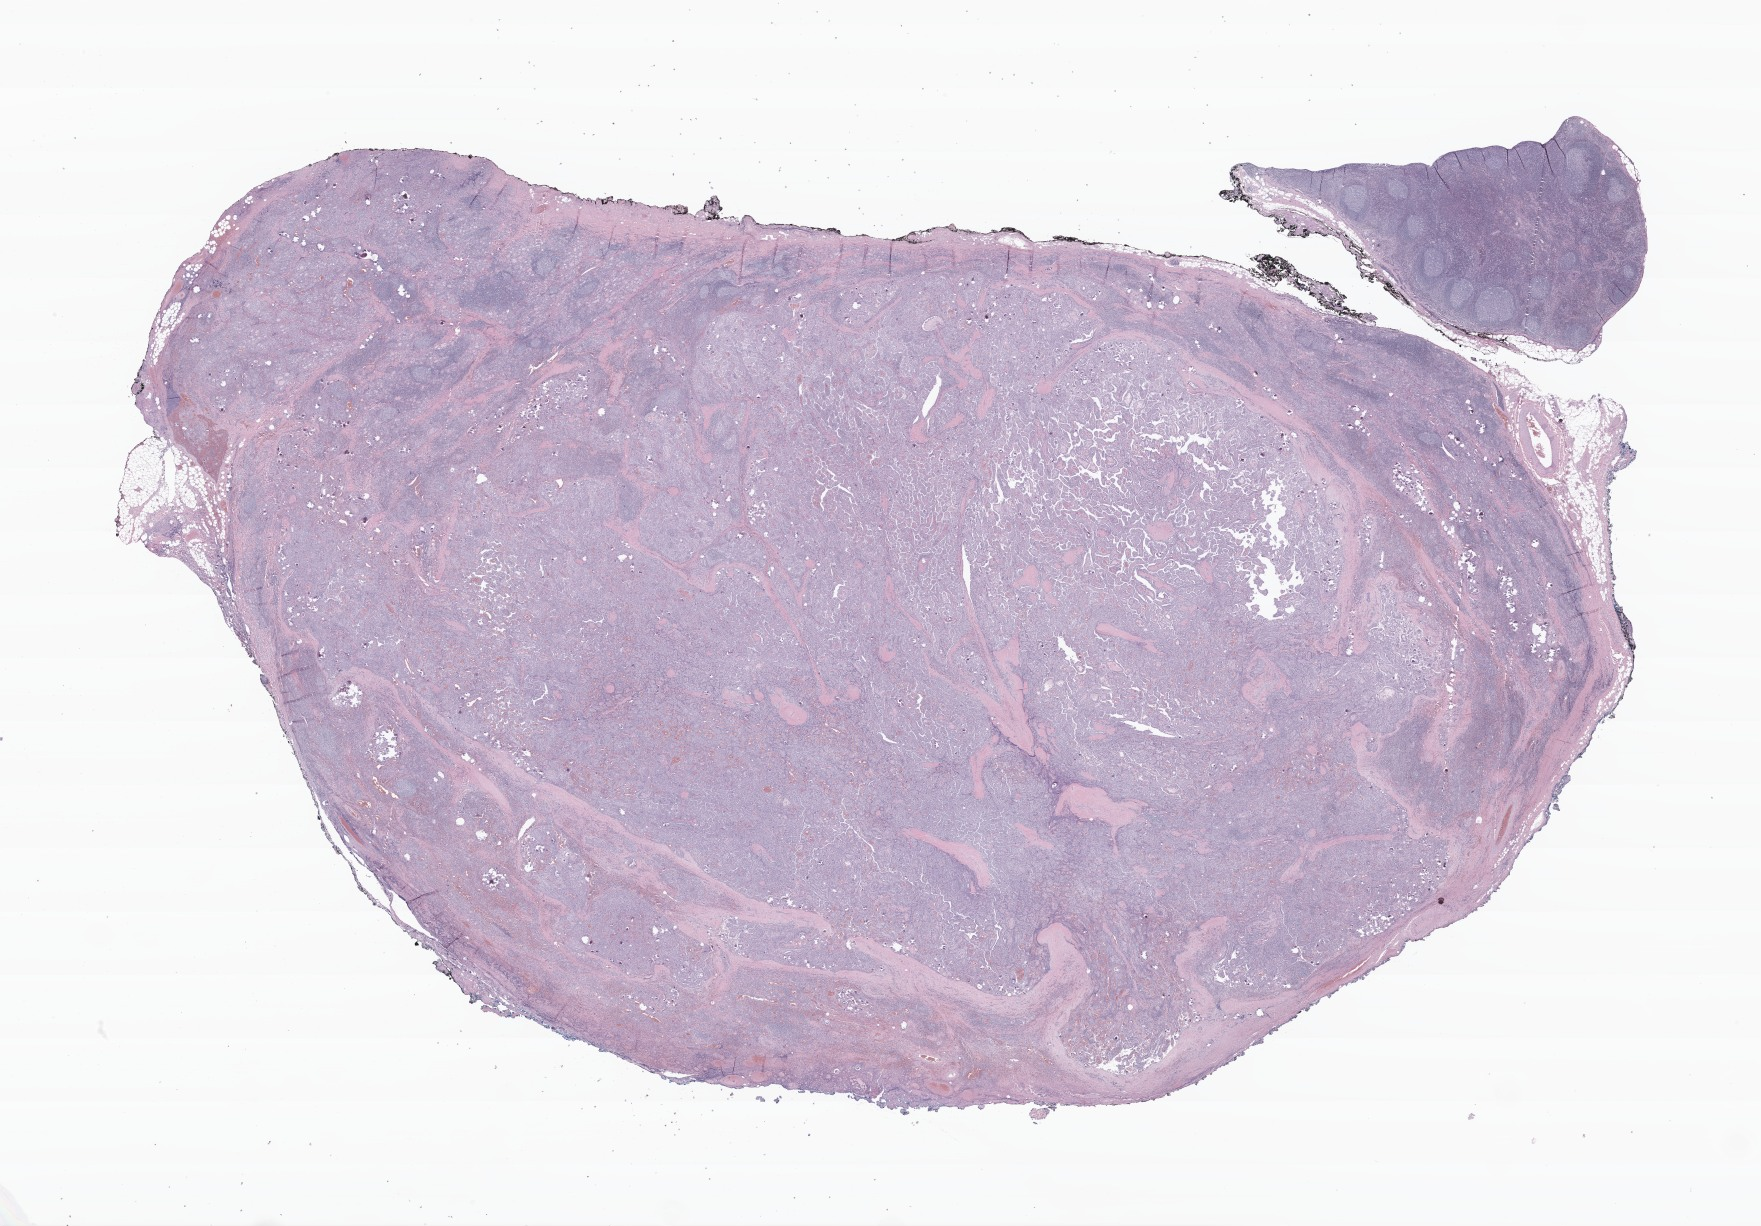
Whole-slide image, haematoxylin and eosin stain of tumor tissue from the thyroid — a low-resolution overview of the entire scanned area, about 29.6 x 20.6 mm; FFPE section. Patient female; age 204 months (17 years).
Diagnosis (ICD-O-3 morphology term): Papillary carcinoma, NOS.